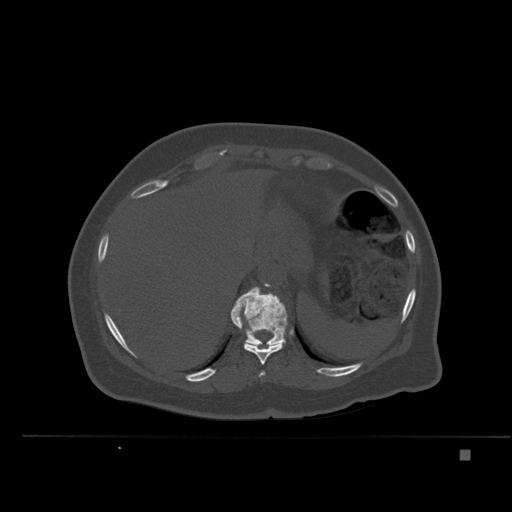
CT including the spine, one axial slice; slice 278 of 477 in the series (ordered by position); bone window (W 1800 / L 400 HU); 1.5 mm slice thickness; 512 × 512 image matrix, field of view 422 × 422 mm. Female patient, age 74 years. Case-level facts recorded for this patient, not image findings: primary cancer: colon.
Annotated regions visible in this slice (semi-automatically segmented with operator editing):
- T10 vertebra: box from (x=234, y=318) to (x=283, y=365) px
- T11 vertebra: (x=230, y=287)–(x=288, y=346)
- T9 vertebra: (x=258, y=371)–(x=266, y=377)